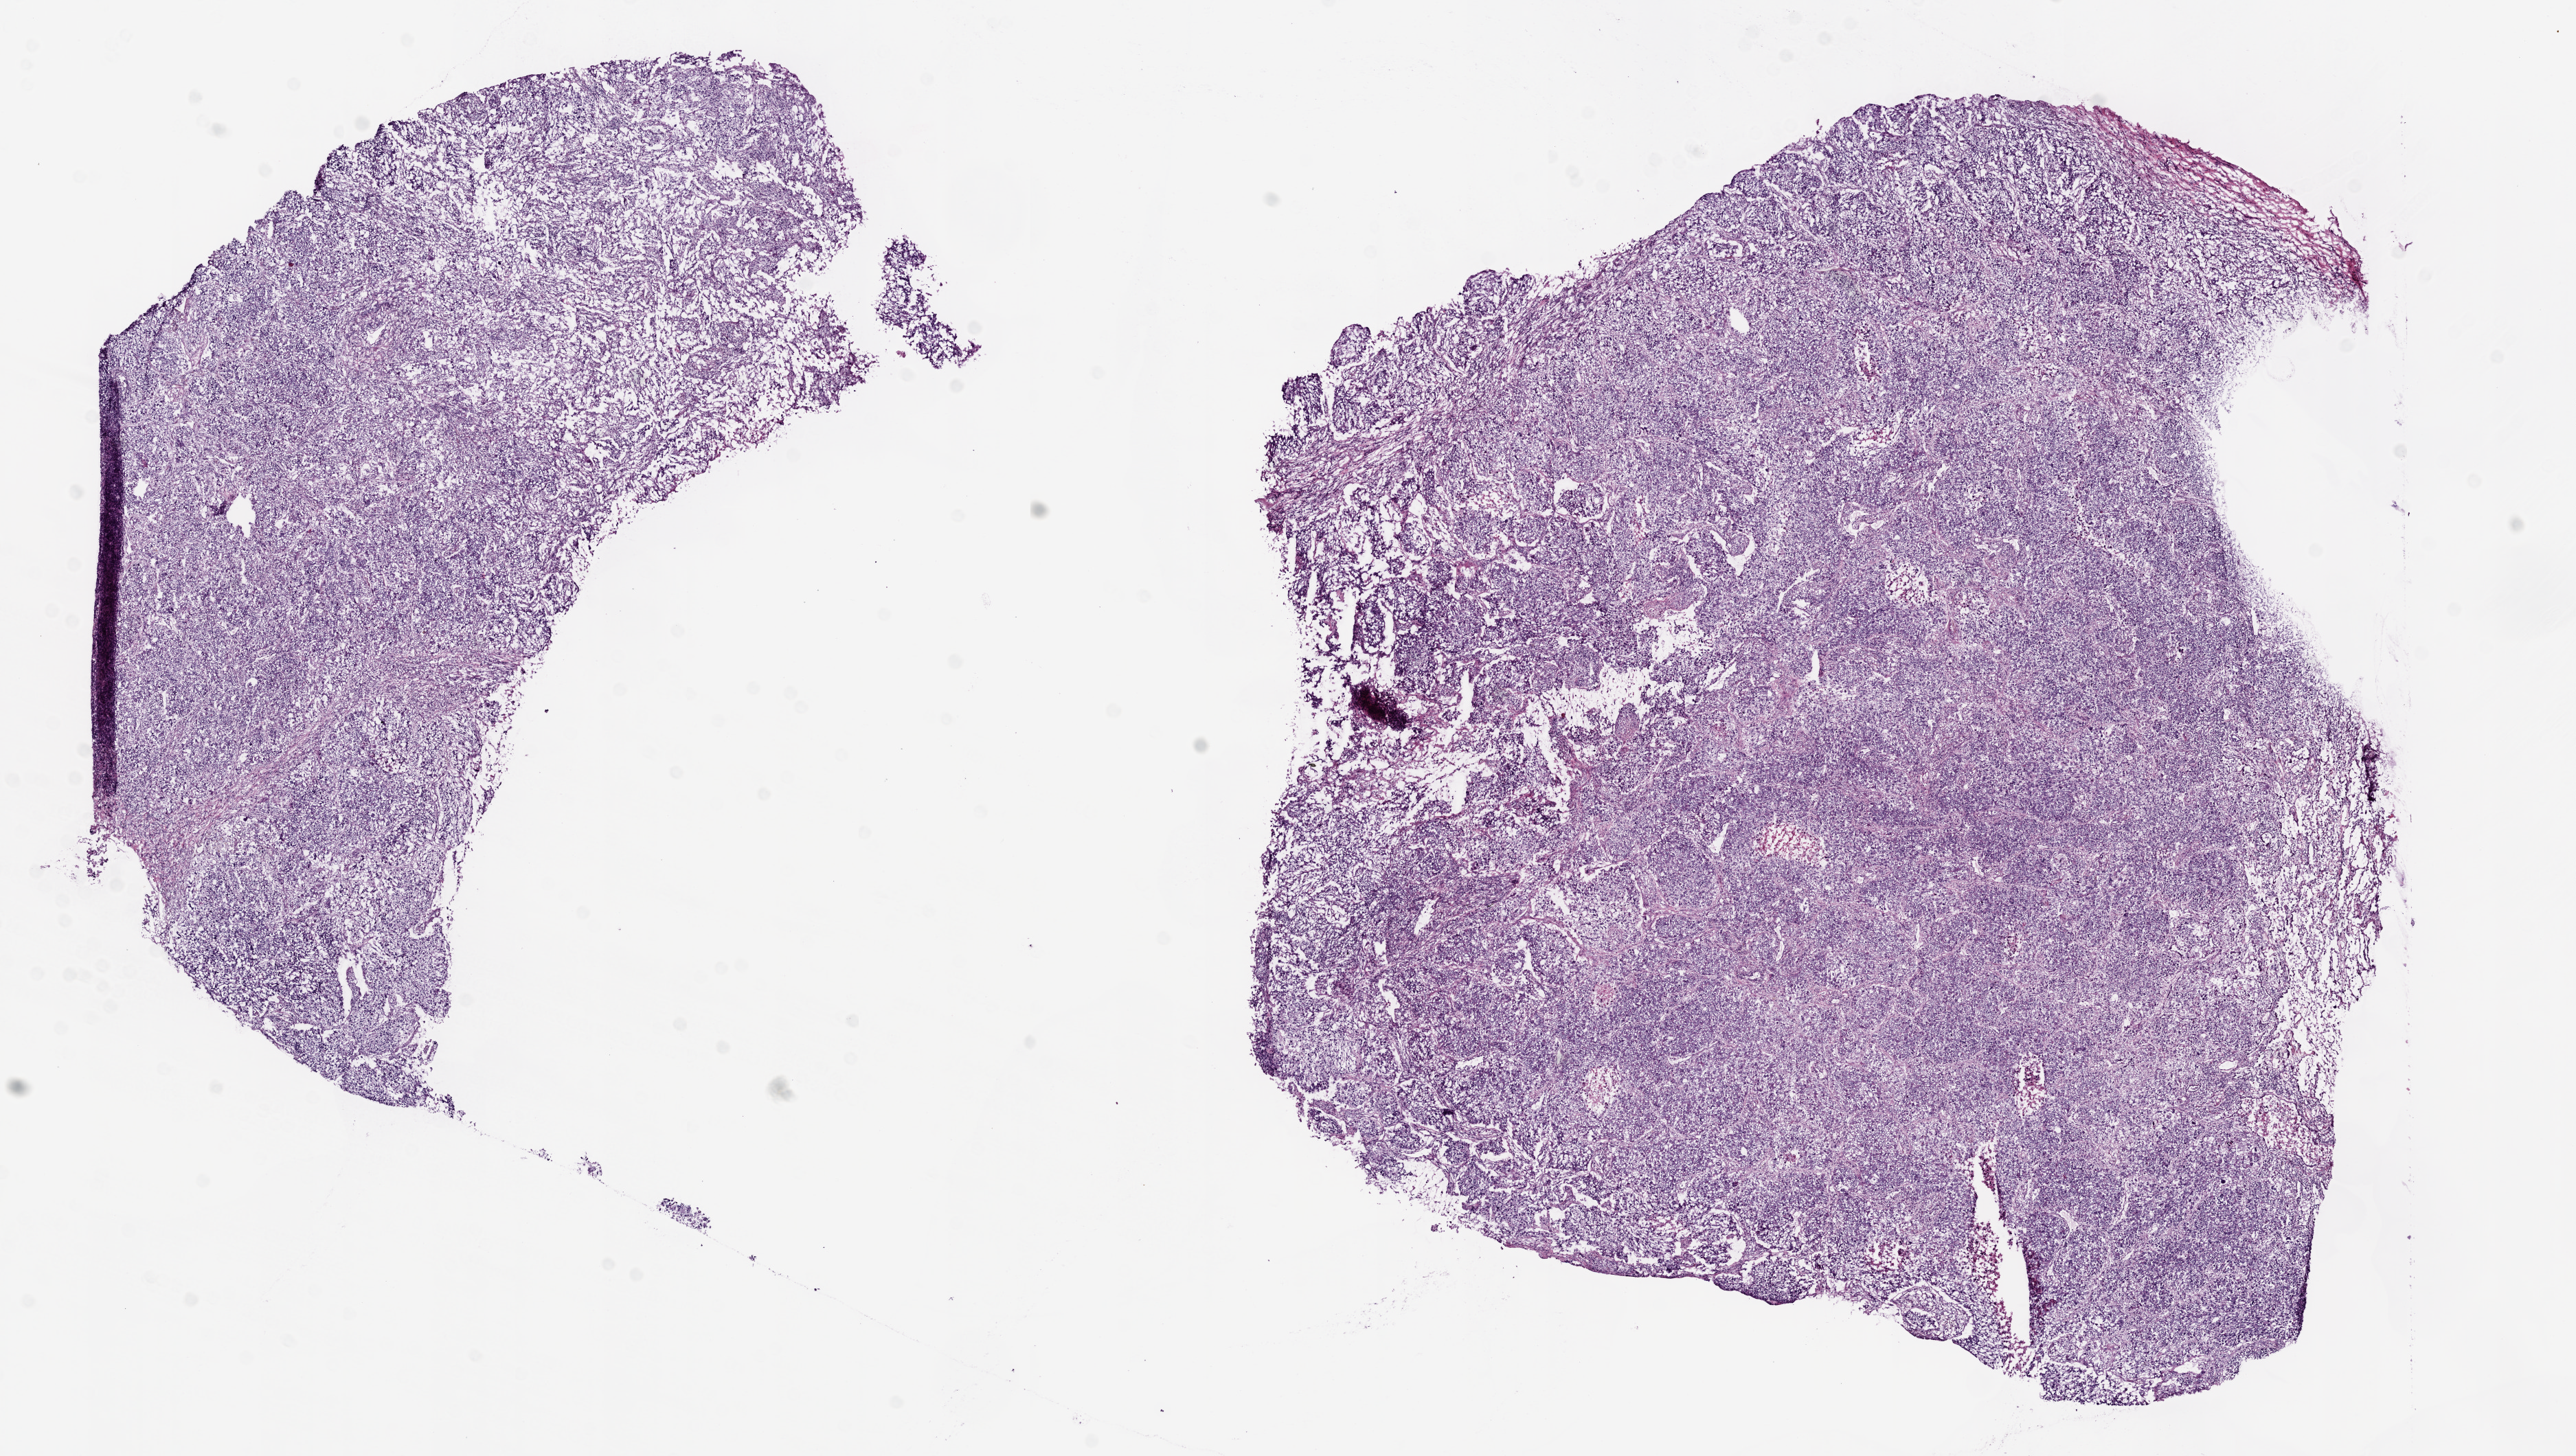
Hematoxylin and eosin (H&E) stained whole-slide image, whole scanned area (about 15.0 x 8.5 mm, acquisition: 20x scan) shown as a low-resolution overview. Frozen section from the bottom of the tissue portion. Sample: primary tumour, lung. Female, age 65 years at initial diagnosis. Pathologist review of this section (percent, as recorded): tumour cells 88%, tumour nuclei 75%, normal cells 0%, stromal cells 10%, necrosis 2%.
AJCC pathologic stage: IIB (6th edition). Diagnosis: Adenocarcinoma with mixed subtypes (upper lobe, lung). Laterality: left.